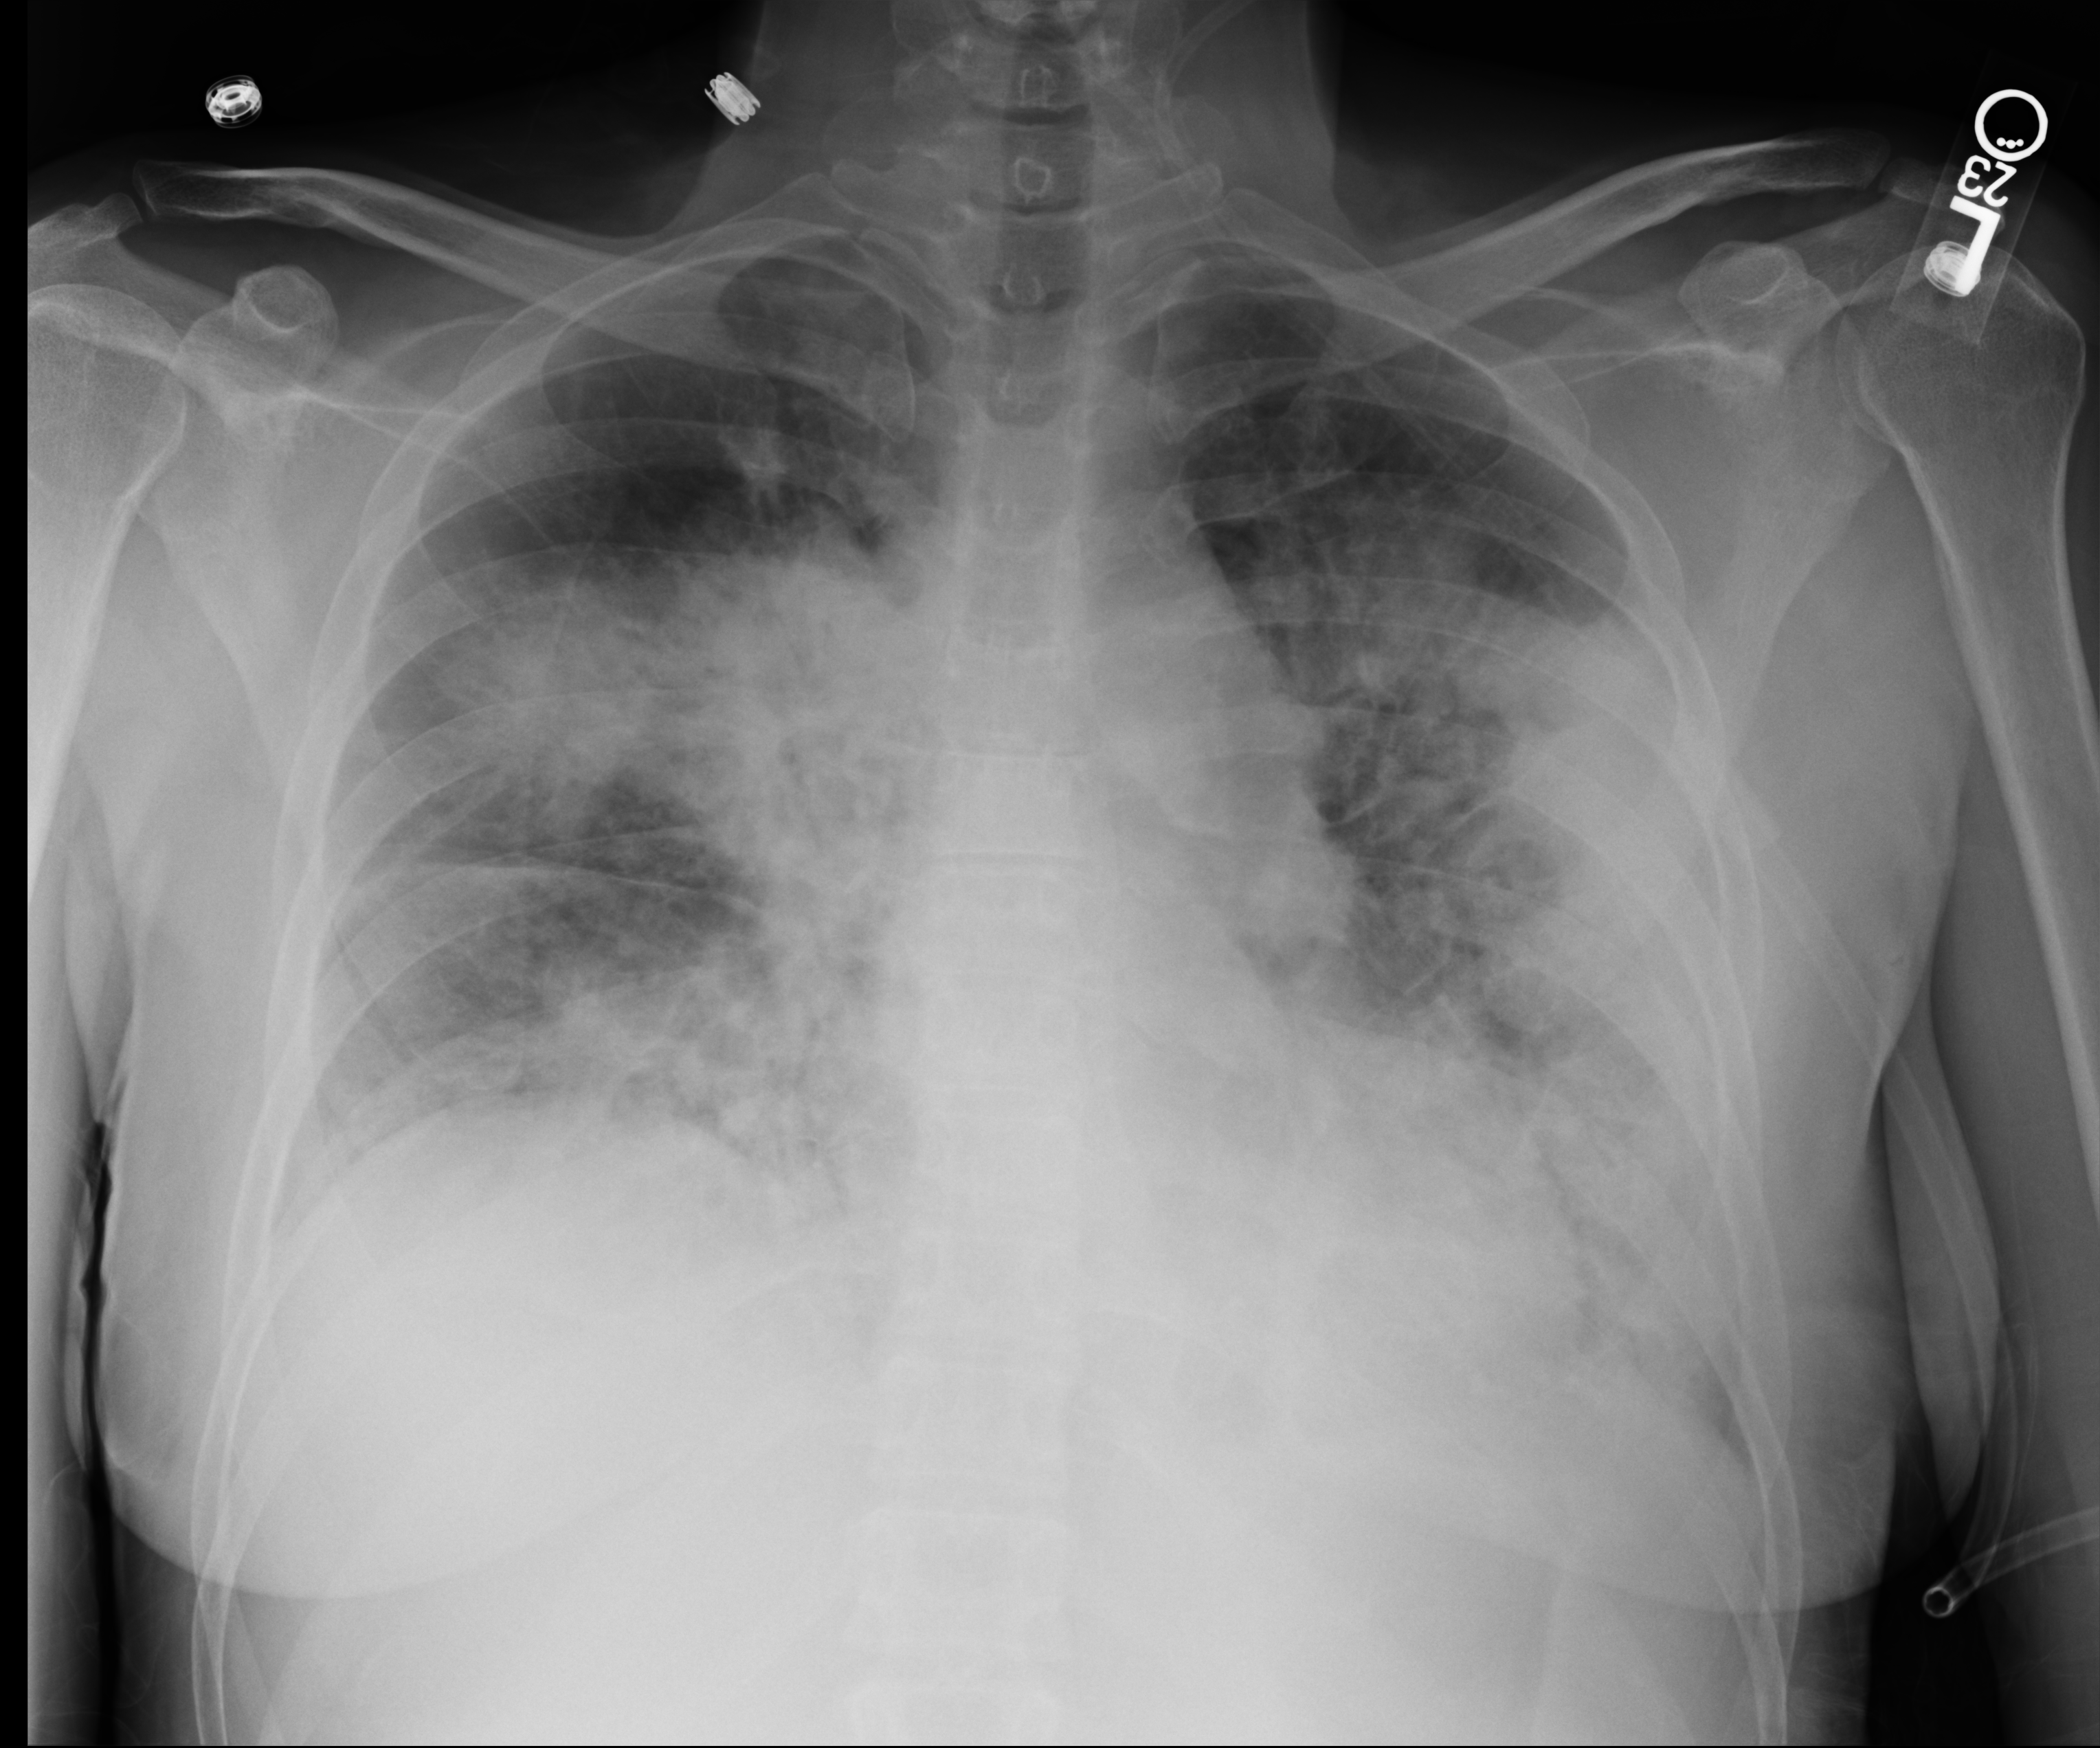
Bedside chest radiograph (computed radiography); anteroposterior (AP) projection. Patient hospitalised with COVID-19; female, aged 18–59 years.
Admission-level facts for this patient (not findings on this image; timing relative to this image not recorded): smoking status (admission record): never; COPD (admission record): no; chronic kidney disease (admission record): no.